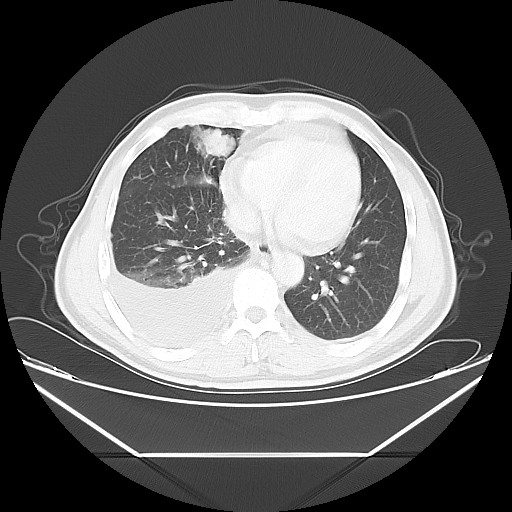
Chest CT, one axial slice; position 18 of 56 along the scan axis; reconstruction kernel LUNG; 120 kVp; lung window (W 1500 / L -600 HU); 512 × 512 image matrix, field of view 412 × 412 mm. Male patient, age 57 years. From the clinical record (not read from this slice): clinical TNM (as recorded): T2 N3 M1.
Annotated regions visible in this slice (bounding box drawn by a radiologist):
- lung tumour (recorded histology: adenocarcinoma): box from (x=180, y=121) to (x=235, y=161) px